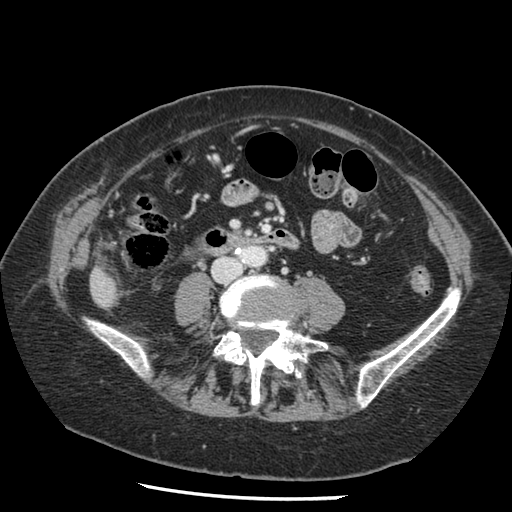
Contrast-enhanced abdominal CT, one axial slice. Position 14 of 148 along the scan axis. Reconstruction kernel STANDARD. Intravenous contrast given. Soft-tissue window (W 400 / L 40 HU). 2.5 mm slice thickness. 512 × 512 image matrix. Female patient, age 85 years. Case-level facts recorded for this patient, not image findings: diagnosis: colorectal cancer liver metastases, imaged before liver resection; multiple liver metastases: no; largest metastasis: 0.9 cm; disease in both lobes: no.
Structures marked on this image (expert manual segmentation):
- liver: bounding box <92,270,117,307> (left, top, right, bottom; pixels)
- planned liver remnant (the part of the liver to remain after resection): <92,270,117,307>